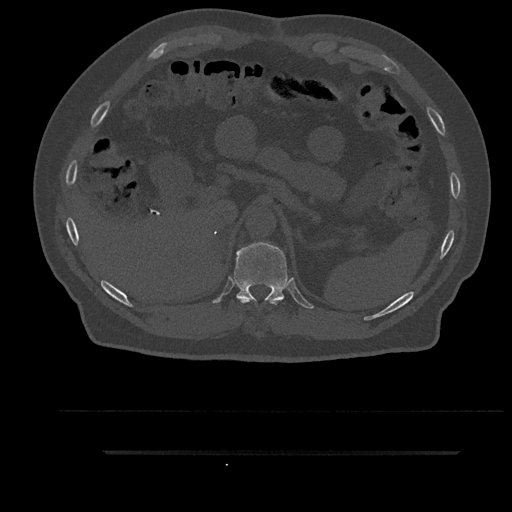
CT including the spine, one axial slice. Slice 327 of 797 in the series (ordered by position). 120 kVp. Bone window (W 1800 / L 400 HU). 512 × 512 image matrix, field of view 432 × 432 mm. Male patient, age 63 years. From the clinical record (not read from this slice): primary cancer: renal; vertebrae with lytic lesions (as recorded): T8.
Outlined on this slice (semi-automatic segmentation, software-assisted and operator-edited):
- T10 vertebra: bounding box (x1, y1, x2, y2) in pixels: (238, 298, 277, 304)
- T11 vertebra: (234, 242, 288, 302)